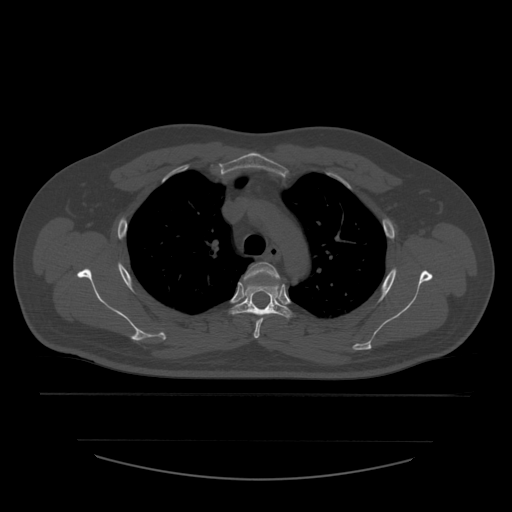
CT including the spine, one axial slice. Slice 422 of 532 in the series (ordered by position). Reconstruction kernel STANDARD. Bone window (W 1800 / L 400 HU). 1.25 mm slice thickness. 512 × 512 image matrix, field of view 441 × 441 mm. Patient age 44 years. Case-level facts recorded for this patient, not image findings: primary cancer: soft tissue sarcoma.
Annotated regions visible in this slice (semi-automatically segmented with operator editing):
- T3 vertebra: bounding box <243,262,282,339> (left, top, right, bottom; pixels)
- T4 vertebra: <231,274,292,319>